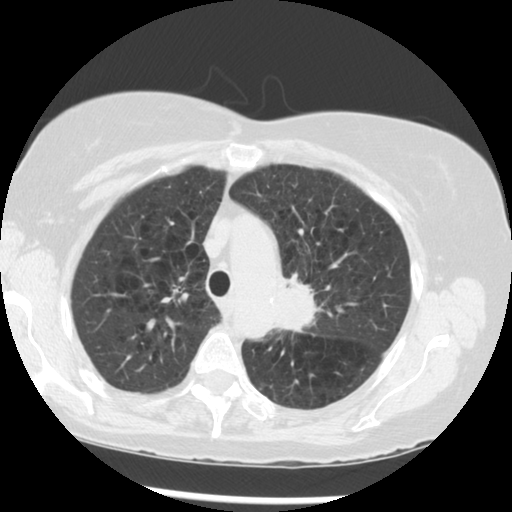
Low-dose screening chest CT, one axial slice; position 213 of 283 along the scan axis; reconstruction kernel STANDARD; 120 kVp; lung window (W 1500 / L -600 HU); 512 × 512 image matrix, field of view 330 × 330 mm.
Outlined on this slice (manually delineated by an expert):
- lesion 1 (tumor, upper lobe of left lung): box from (x=276, y=274) to (x=317, y=331) px